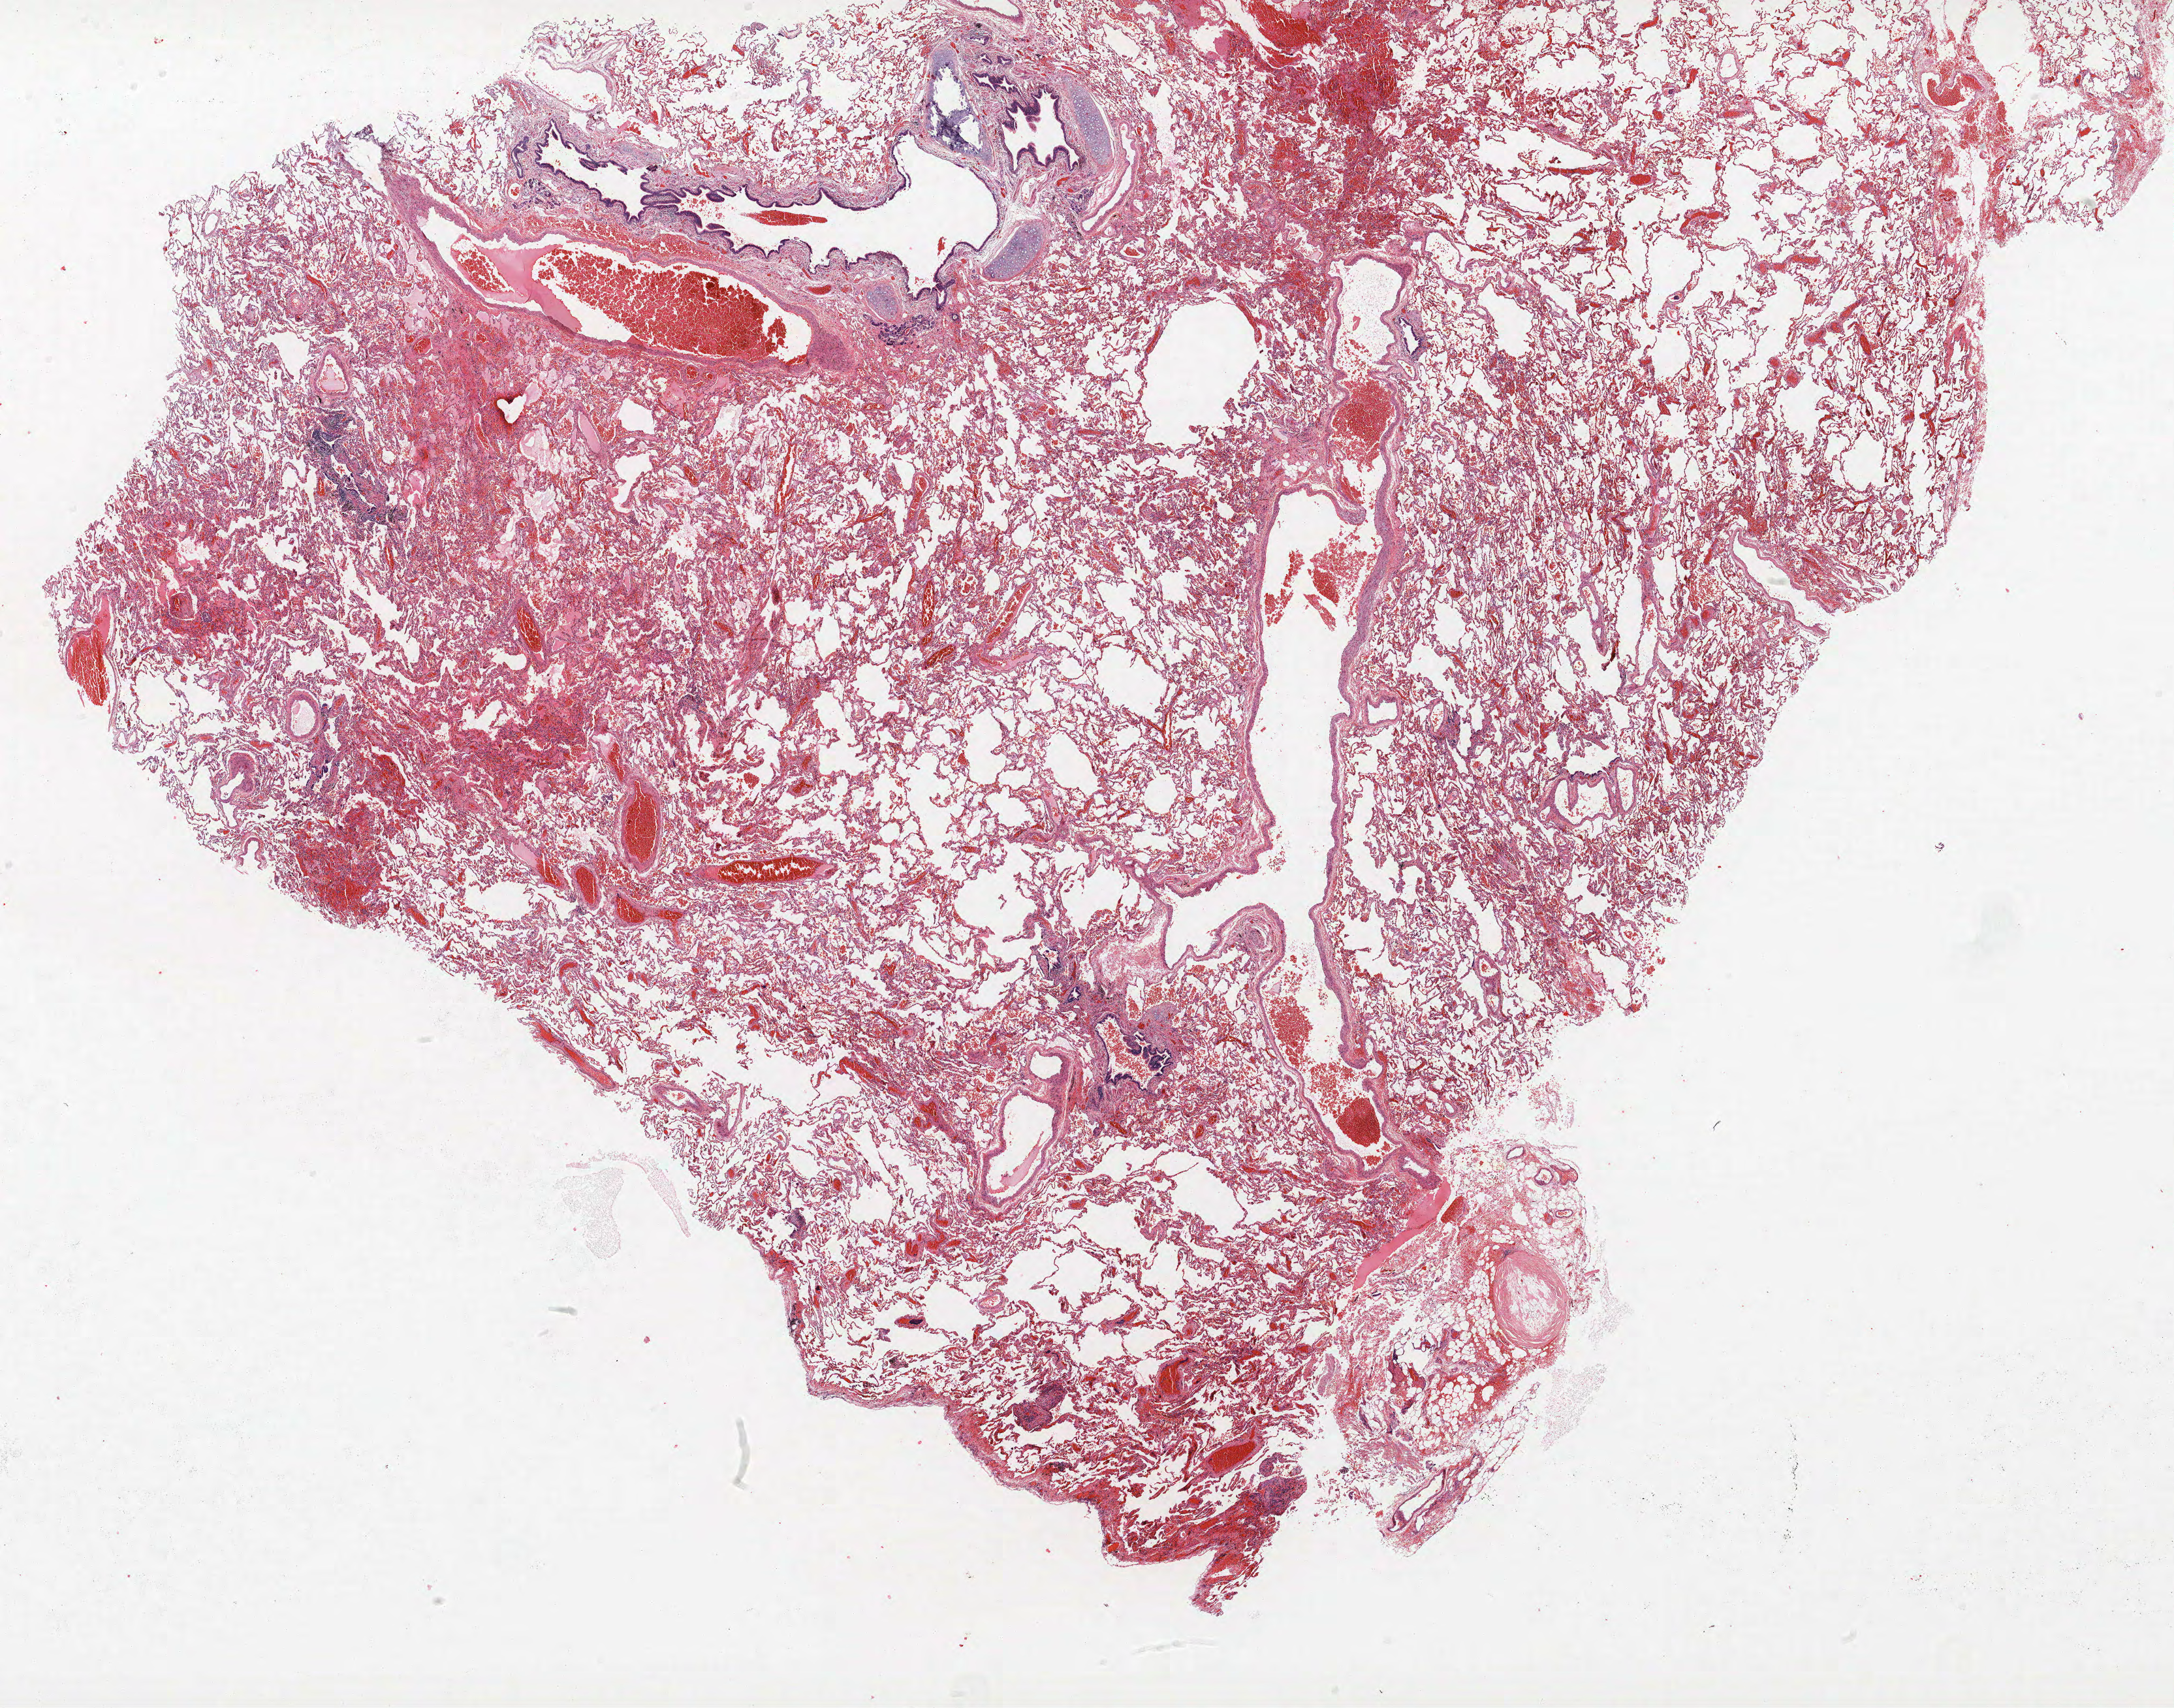
Hematoxylin and eosin (H&E) stained whole-slide image, shown as a low-resolution overview of the whole scanned area (about 26.6 x 20.9 mm), FFPE section, lung. Male, age 61 at enrolment. Grade: poorly differentiated (G3).
Stage (AJCC 6th edition): IB. Tumour size (pathology): 35 mm. Participant's lung-cancer diagnosis: Adenocarcinoma, NOS (ICD-O-3 8140/3). Primary tumour location (clinical record): left upper lobe.